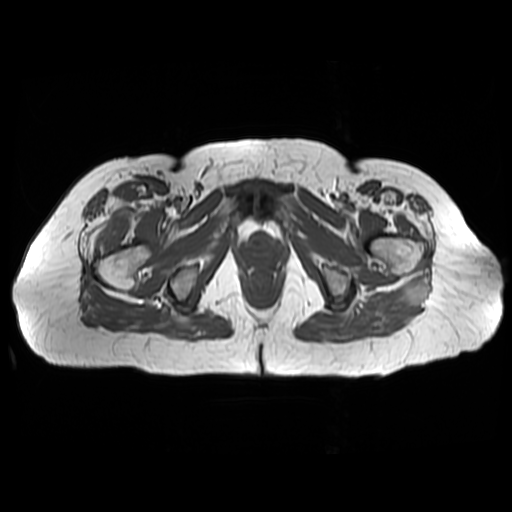
MRI of an extremity soft-tissue mass, one axial slice. Position 41 of 48 along the scan axis. 512 × 512 image matrix. Female patient. Case-level facts recorded for this patient, not image findings: histological type: pleiomorphic undifferentiated sarcoma; grade: high; site of the primary tumour: right quadricep.
Structures marked on this image (expert manual segmentation):
- gross tumour volume including surrounding oedema: box from (x=95, y=215) to (x=122, y=256) px